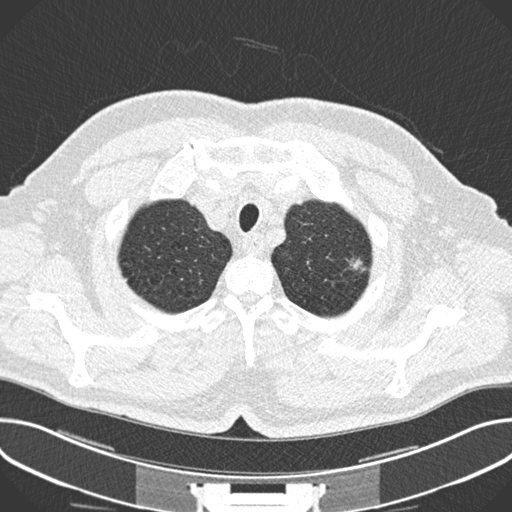
Low-dose screening chest CT, one axial slice; position 217 of 244 along the scan axis; 120 kVp; lung window (W 1500 / L -600 HU); 512 × 512 image matrix.
Structures marked on this image (manually delineated by an expert):
- lesion 1 (tumor, upper lobe of left lung): bounding box [x1, y1, x2, y2] px = [347, 258, 366, 272]